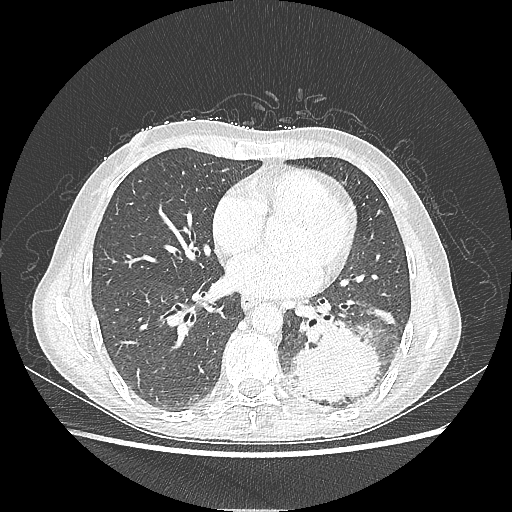
Chest CT, one axial slice; slice 97 of 220 in the series (ordered by position); 80 kVp; lung window (W 1500 / L -600 HU); 1.25 mm slice thickness; 512 × 512 image matrix, field of view 360 × 360 mm. Female patient, age 53 years. From the clinical record (not read from this slice): clinical TNM (as recorded): T3 N0 M0.
Structures marked on this image (bounding box drawn by a radiologist):
- lung tumour (recorded histology: adenocarcinoma): bounding box (x1, y1, x2, y2) in pixels: (279, 315, 381, 404)